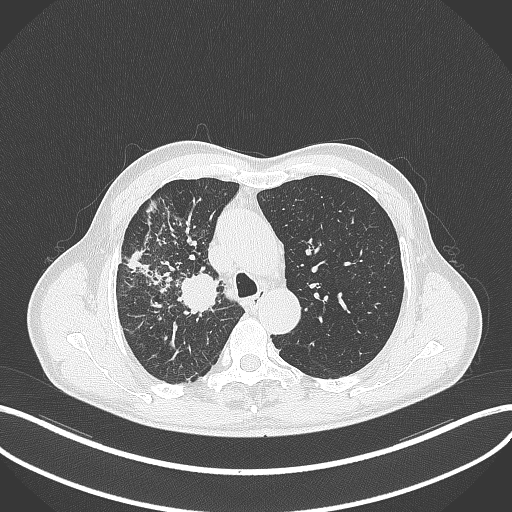
Chest CT, one axial slice. Position 344 of 490 along the scan axis. Reconstruction kernel B70f. 120 kVp. Lung window (W 1500 / L -600 HU). 512 × 512 image matrix. Patient: male, 69 years. Case-level facts recorded for this patient, not image findings: clinical TNM (as recorded): T2a N0 M0.
Annotated regions visible in this slice (rectangle marked by the reading radiologist):
- lung tumour (recorded histology: adenocarcinoma): bounding box (x1, y1, x2, y2) in pixels: (176, 273, 223, 313)